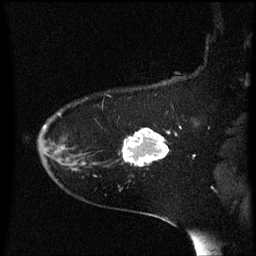
Breast MRI (dynamic contrast-enhanced), one sagittal slice. Dynamic contrast-enhanced series, image 2 of 3 at this slice position (ordered by acquisition). 1.5 T. TE 4.2 ms, TR 8.4 ms. 2 mm slice thickness. 256 × 256 image matrix, field of view 200 × 200 mm. Patient: female, 54 years. From the clinical record (not read from this slice): setting: breast cancer imaged before/during neoadjuvant chemotherapy; receptor status: HR-positive, HER2-negative.
Annotated regions visible in this slice (semi-automatically segmented with operator editing):
- analysis volume of interest (the breast-tissue region the enhancement analysis was run in; not a lesion): box from (x=124, y=128) to (x=171, y=167) px
- tumour enhancement mask (voxels above the 70 % enhancement threshold inside the analysis volume of interest): (x=124, y=130)–(x=170, y=167)